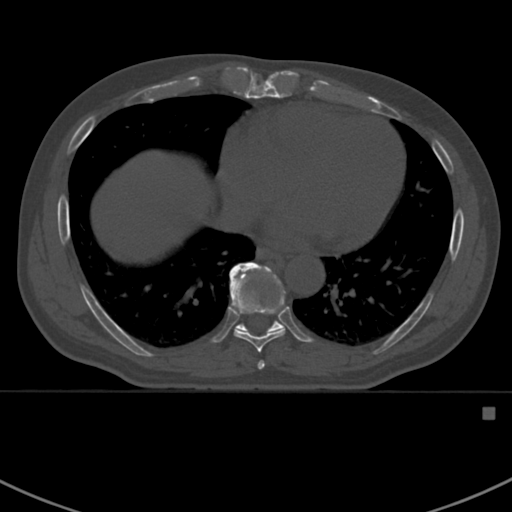
CT including the spine, one axial slice. Position 395 of 412 along the scan axis. Reconstruction kernel Br40s. 120 kVp. Bone window (W 1800 / L 400 HU). 512 × 512 image matrix, field of view 358 × 358 mm. Male patient, age 59 years. From the clinical record (not read from this slice): primary cancer: prostate.
Annotated regions visible in this slice (semi-automatic segmentation, software-assisted and operator-edited):
- T7 vertebra: bounding box <257,360,265,370> (left, top, right, bottom; pixels)
- T8 vertebra: <230,291,285,353>
- T9 vertebra: <230,262,289,333>